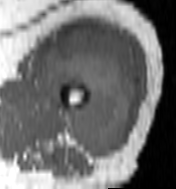
MRI of an extremity soft-tissue mass, one axial slice. Position 70 of 100 along the scan axis. MR volume resampled by the dataset authors to the PET/CT grid (not the native acquisition matrix). 3.27 mm slice thickness. 176 × 189 image matrix, field of view 172 × 185 mm. Female patient. Case-level facts recorded for this patient, not image findings: histological type: undifferentiated – high grade; grade: high; site of the primary tumour: left thigh.
Structures marked on this image (expert contour drawn on MRI and transferred to this co-registered scan by the dataset authors):
- gross tumour volume including surrounding oedema: bounding box <44,30,138,158> (left, top, right, bottom; pixels)
- gross tumour volume (mass): <44,30,138,158>